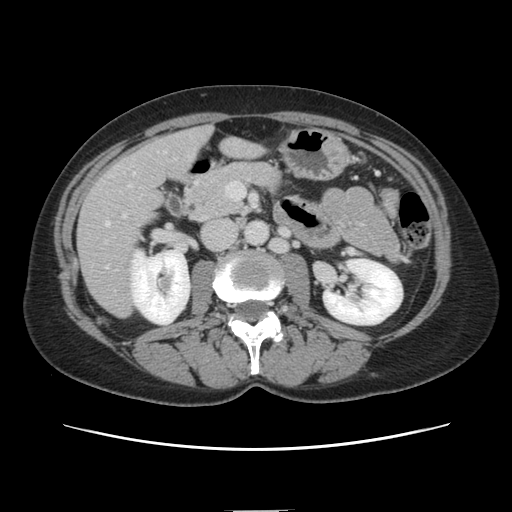
Contrast-enhanced abdominal CT, one axial slice. Position 49 of 141 along the scan axis. 120 kVp. Soft-tissue window (W 400 / L 40 HU). 2.5 mm slice thickness. 512 × 512 image matrix, field of view 350 × 350 mm. Female patient, age 63 years. From the clinical record (not read from this slice): diagnosis: colorectal cancer liver metastases, imaged before liver resection; multiple liver metastases: yes; largest metastasis: 3.2 cm.
Annotated regions visible in this slice (outlined manually by an expert reader):
- liver: bounding box [x1, y1, x2, y2] px = [79, 129, 258, 316]
- planned liver remnant (the part of the liver to remain after resection): [179, 128, 258, 167]